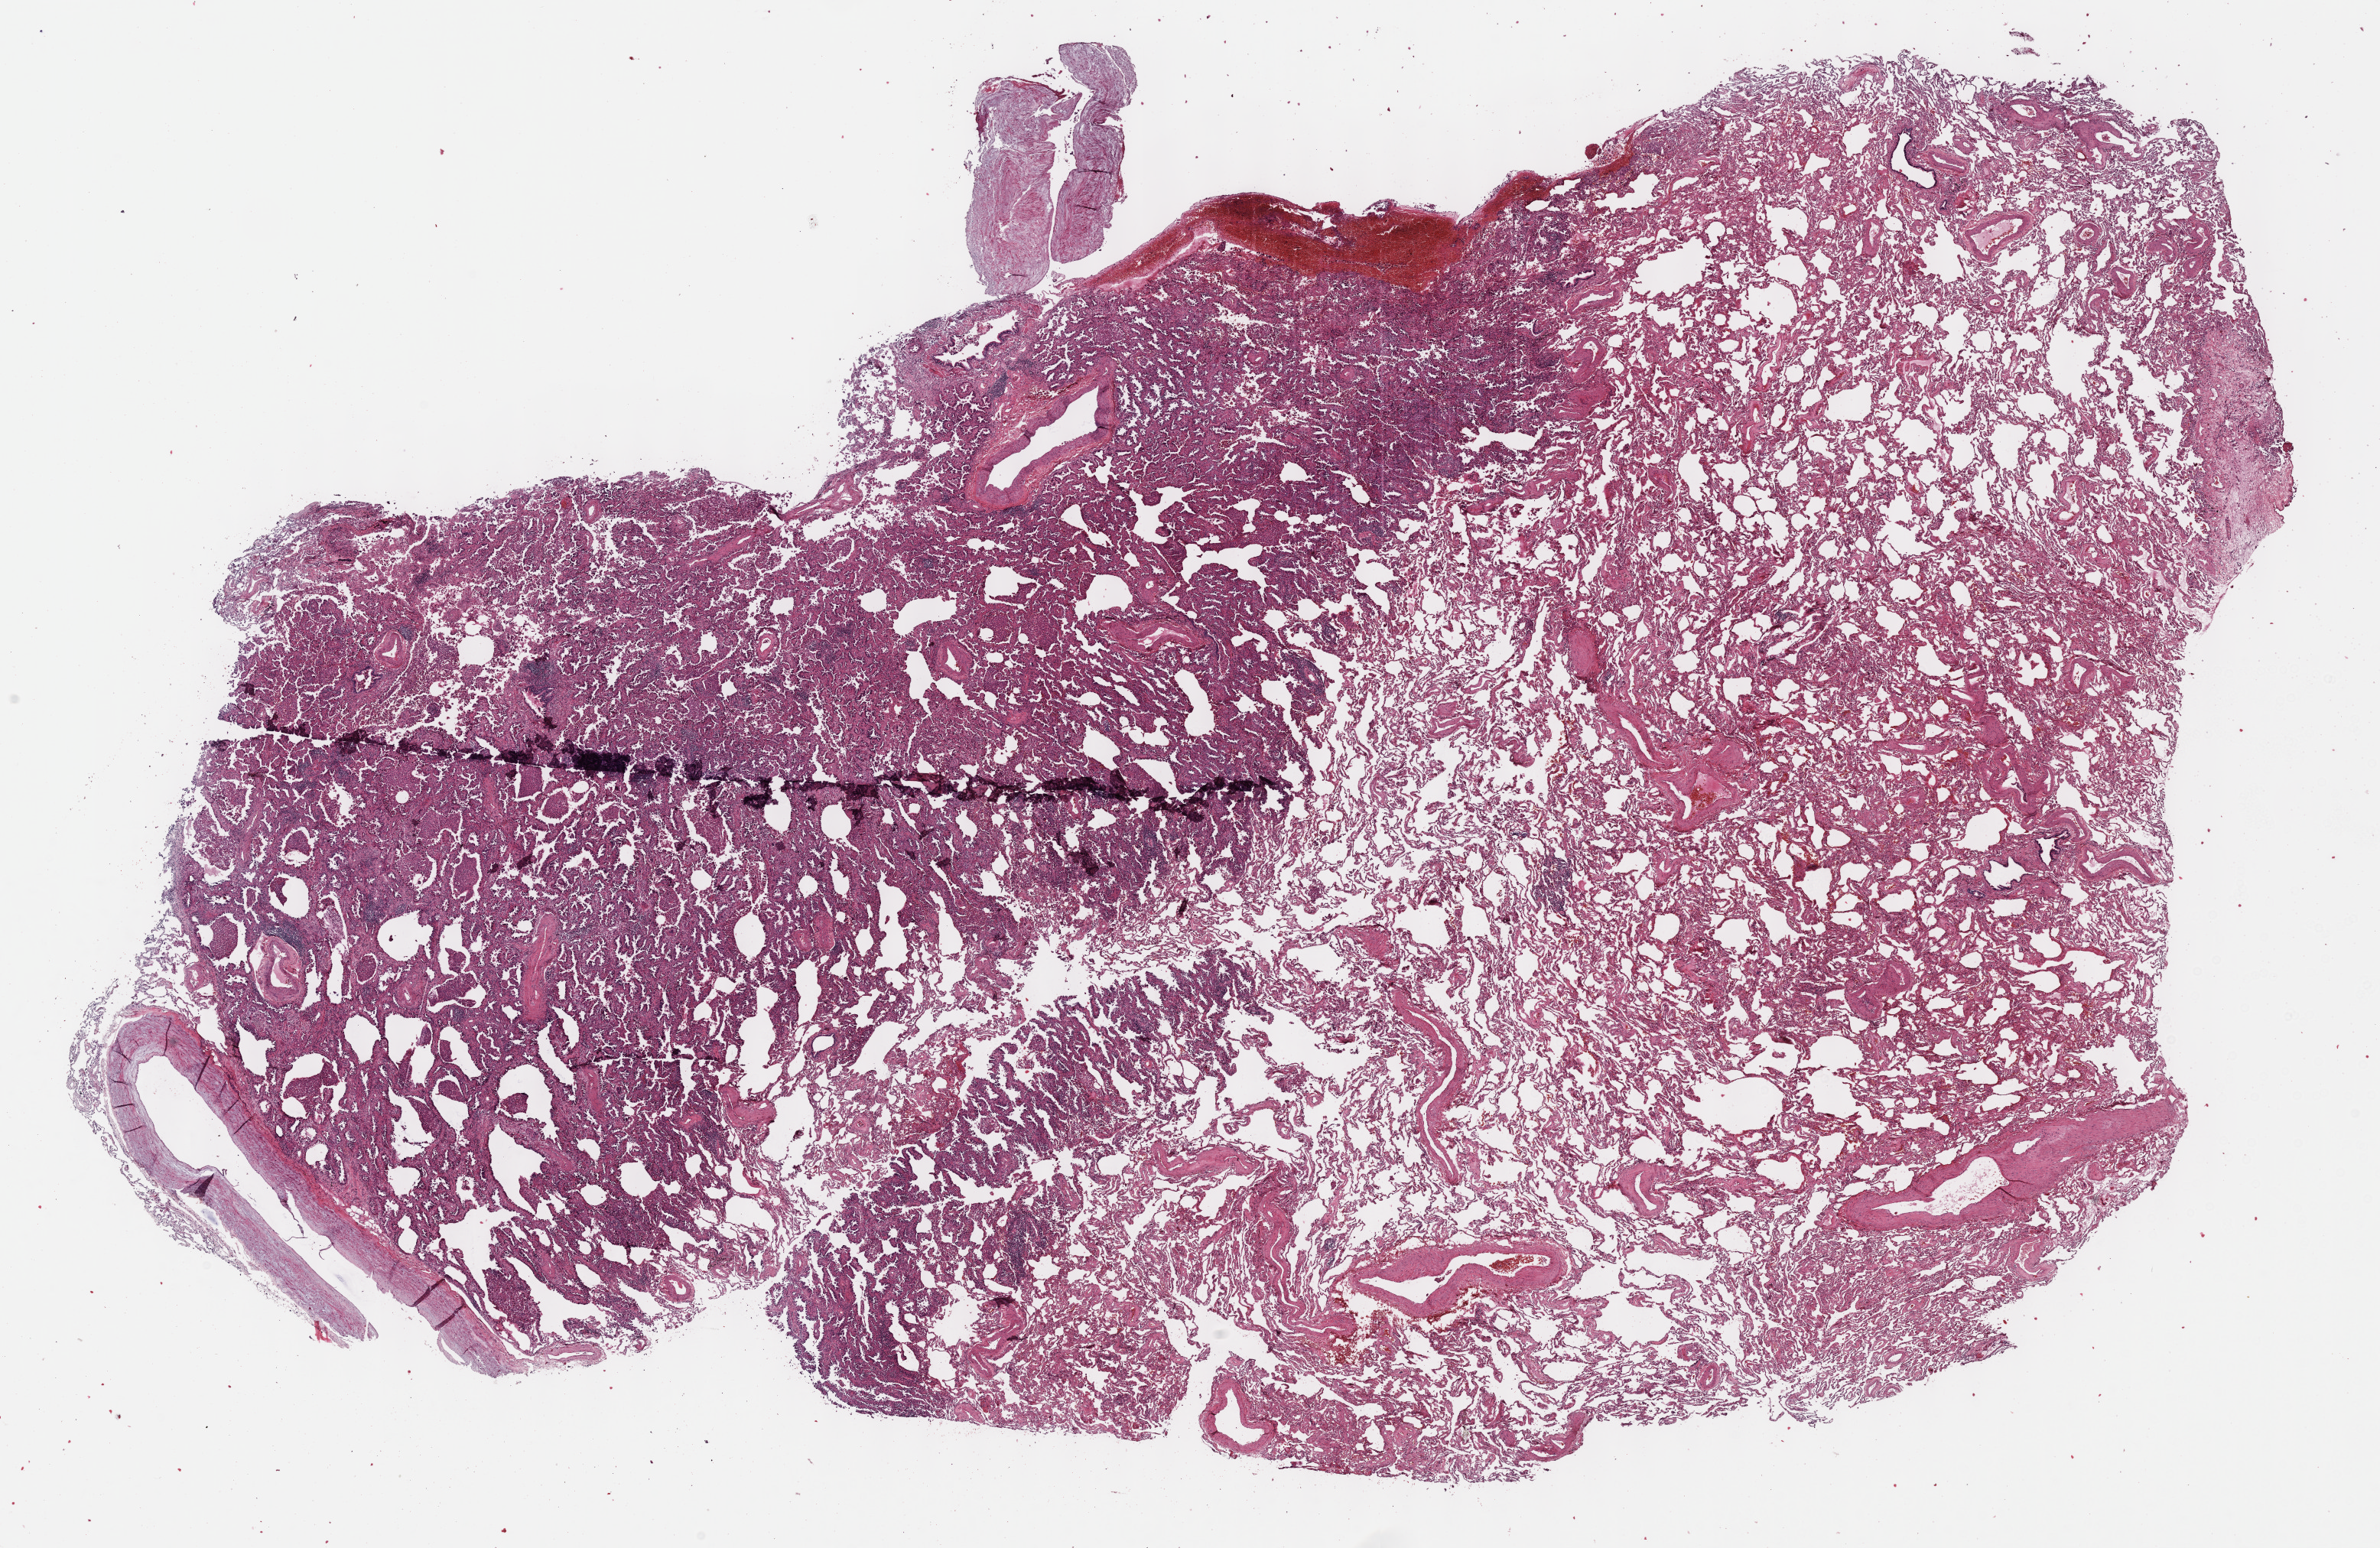
Hematoxylin and eosin (H&E) stained whole-slide image — shown as a low-resolution overview of the whole scanned area (about 25.2 x 16.4 mm, acquisition: 40x scan); formalin-fixed paraffin-embedded (FFPE) diagnostic section; lung, primary tumour sample. Female, age 74 years at initial diagnosis.
TNM: T1 N0 MX. Laterality: left. Diagnosis: Adenocarcinoma, NOS. AJCC pathologic stage: IA (6th edition).